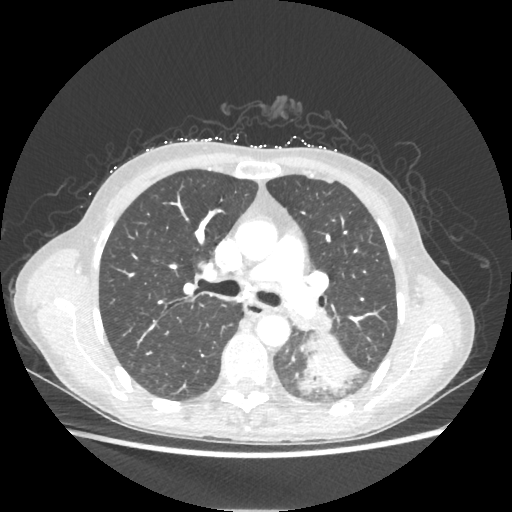
Chest CT, one axial slice; position 136 of 221 along the scan axis; reconstruction kernel STANDARD; 80 kVp; lung window (W 1500 / L -600 HU); 1.25 mm slice thickness; 512 × 512 image matrix, field of view 360 × 360 mm. Female patient, age 53 years. From the clinical record (not read from this slice): clinical TNM (as recorded): T3 N0 M0.
Outlined on this slice (bounding box drawn by a radiologist):
- lung tumour (recorded histology: adenocarcinoma): bounding box <298,339,360,393> (left, top, right, bottom; pixels)